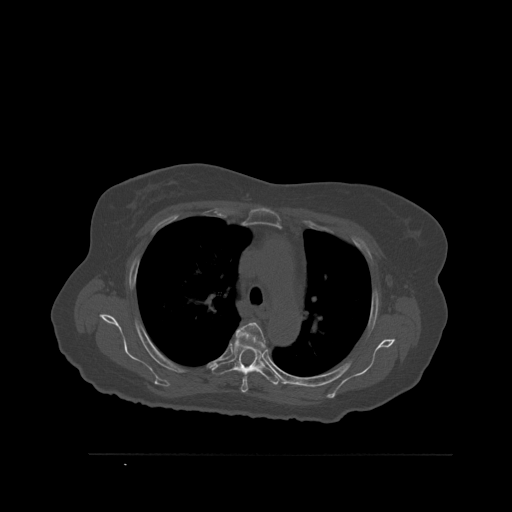
CT including the spine, one axial slice. Slice 400 of 527 in the series (ordered by position). Bone window (W 1800 / L 400 HU). 1.5 mm slice thickness. 512 × 512 image matrix, field of view 470 × 470 mm. Patient: female, 73 years. Case-level facts recorded for this patient, not image findings: primary cancer: breast.
Structures marked on this image (semi-automatic segmentation, software-assisted and operator-edited):
- T4 vertebra: bounding box [x1, y1, x2, y2] px = [236, 322, 267, 393]
- T5 vertebra: [212, 341, 280, 386]